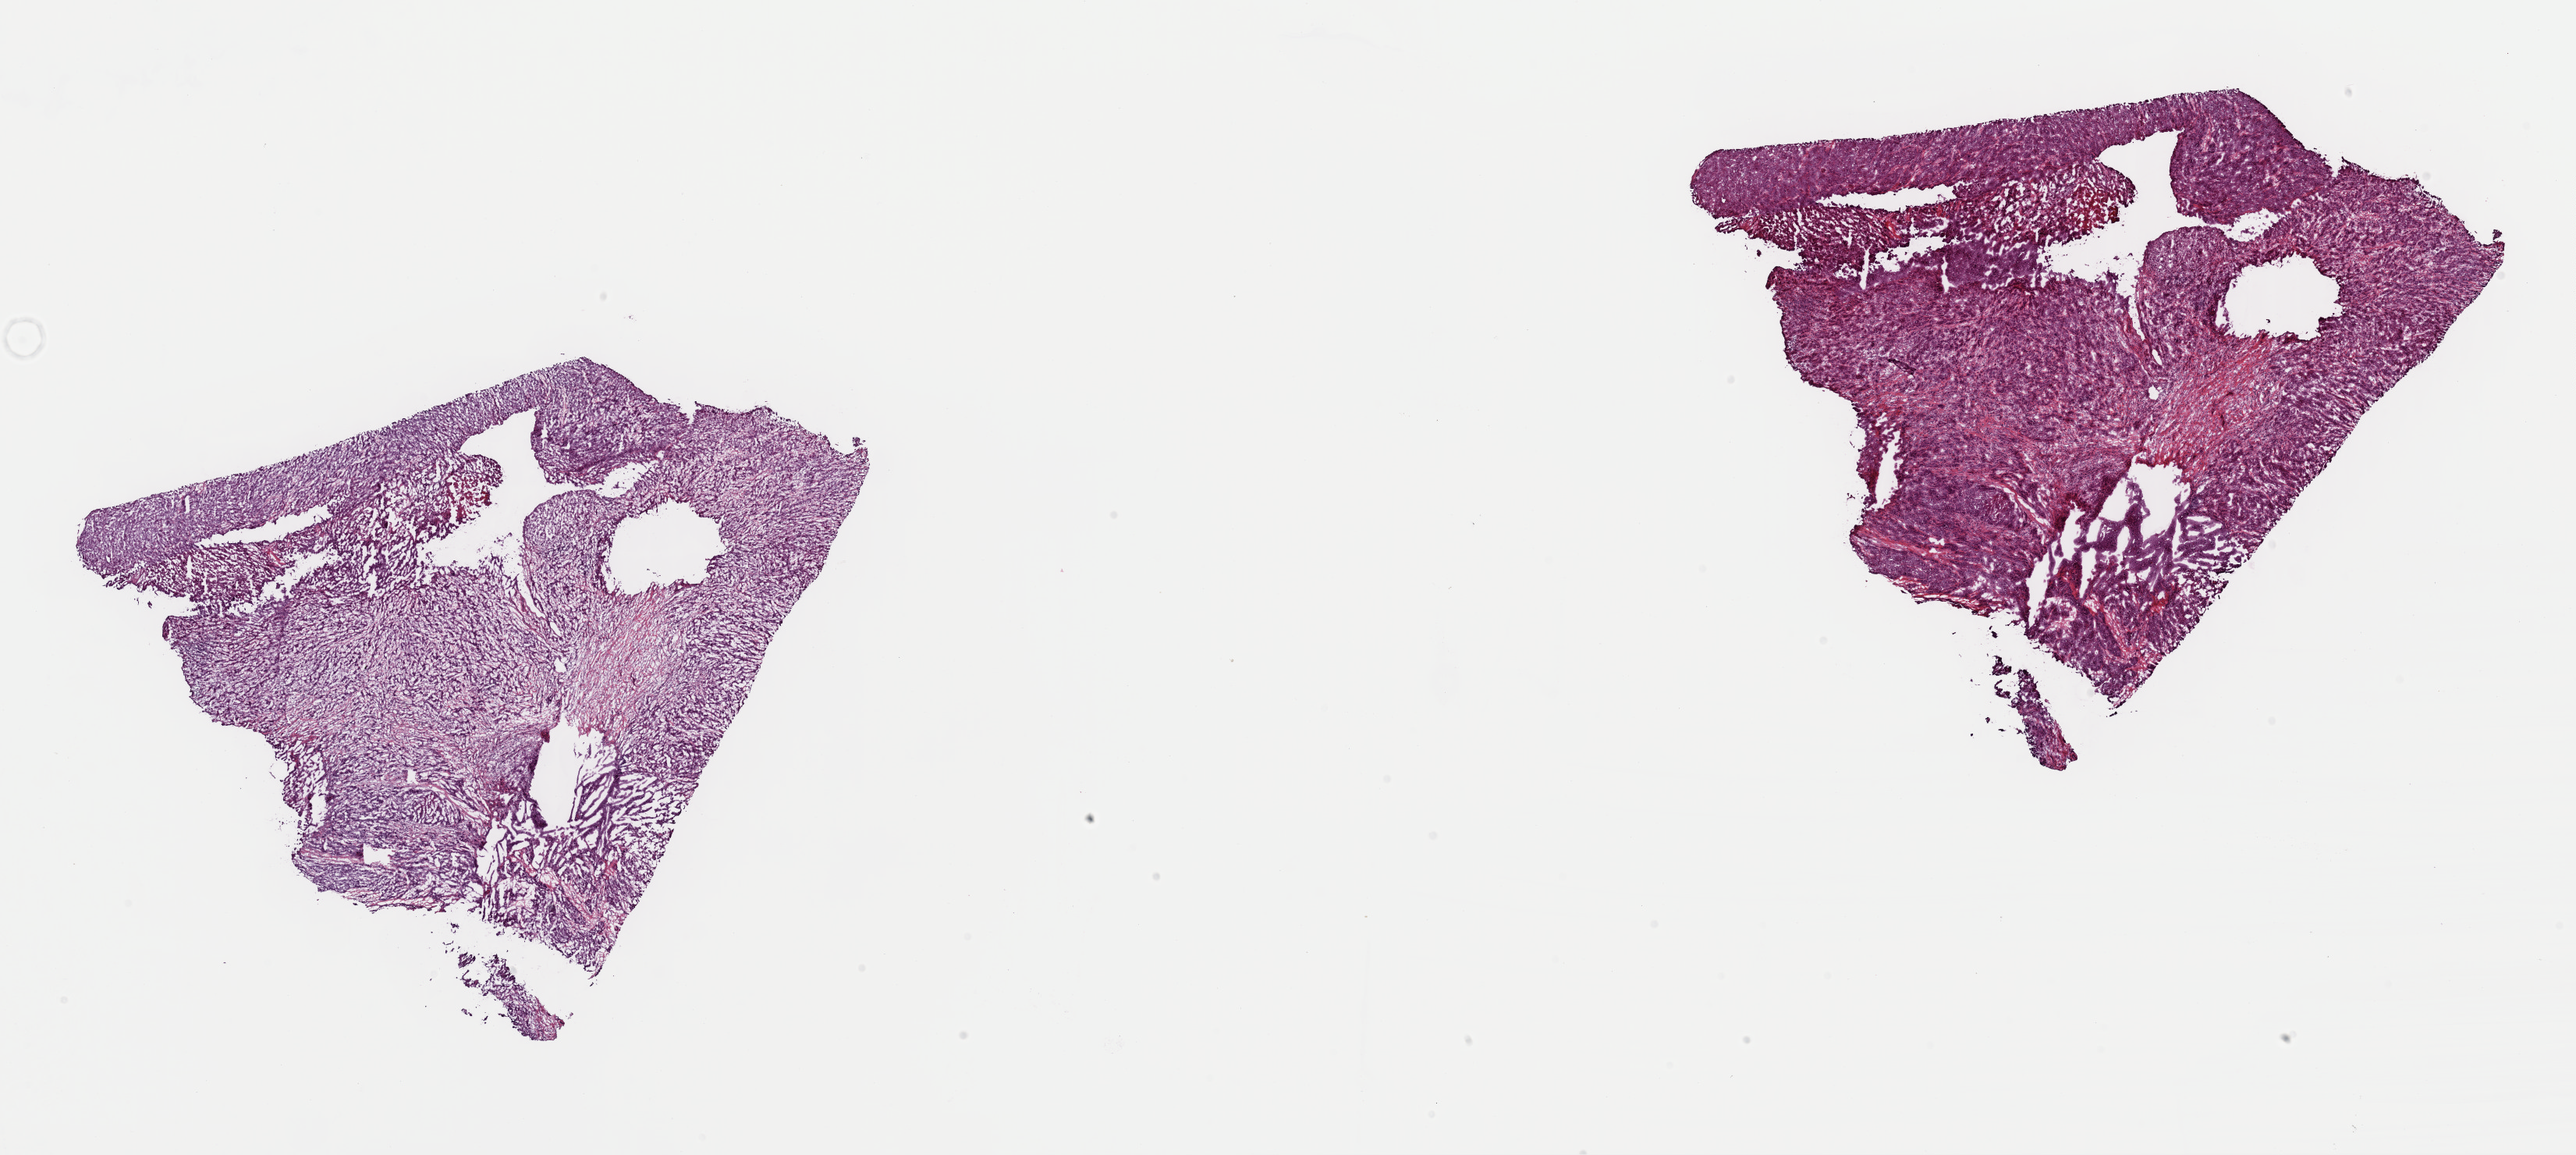
H&E-stained whole-slide image, a low-resolution overview of the entire scanned area, about 26.1 x 11.7 mm (slide scanned at 40x), frozen section from the top of the tissue portion, primary tumour sample from the liver. Male, age 58 years at initial diagnosis. Histologic grade: G3 (poorly differentiated). Slide review estimates, as recorded: tumour cells 70%, tumour nuclei 60%, normal cells 0%, stromal cells 25%, necrosis 5%. Inflammatory infiltration, as recorded: lymphocyte infiltration 100%, monocyte infiltration 0%, neutrophil infiltration 0%.
• AJCC pathologic stage: II (7th edition)
• pathologic diagnosis: Hepatocellular carcinoma, NOS